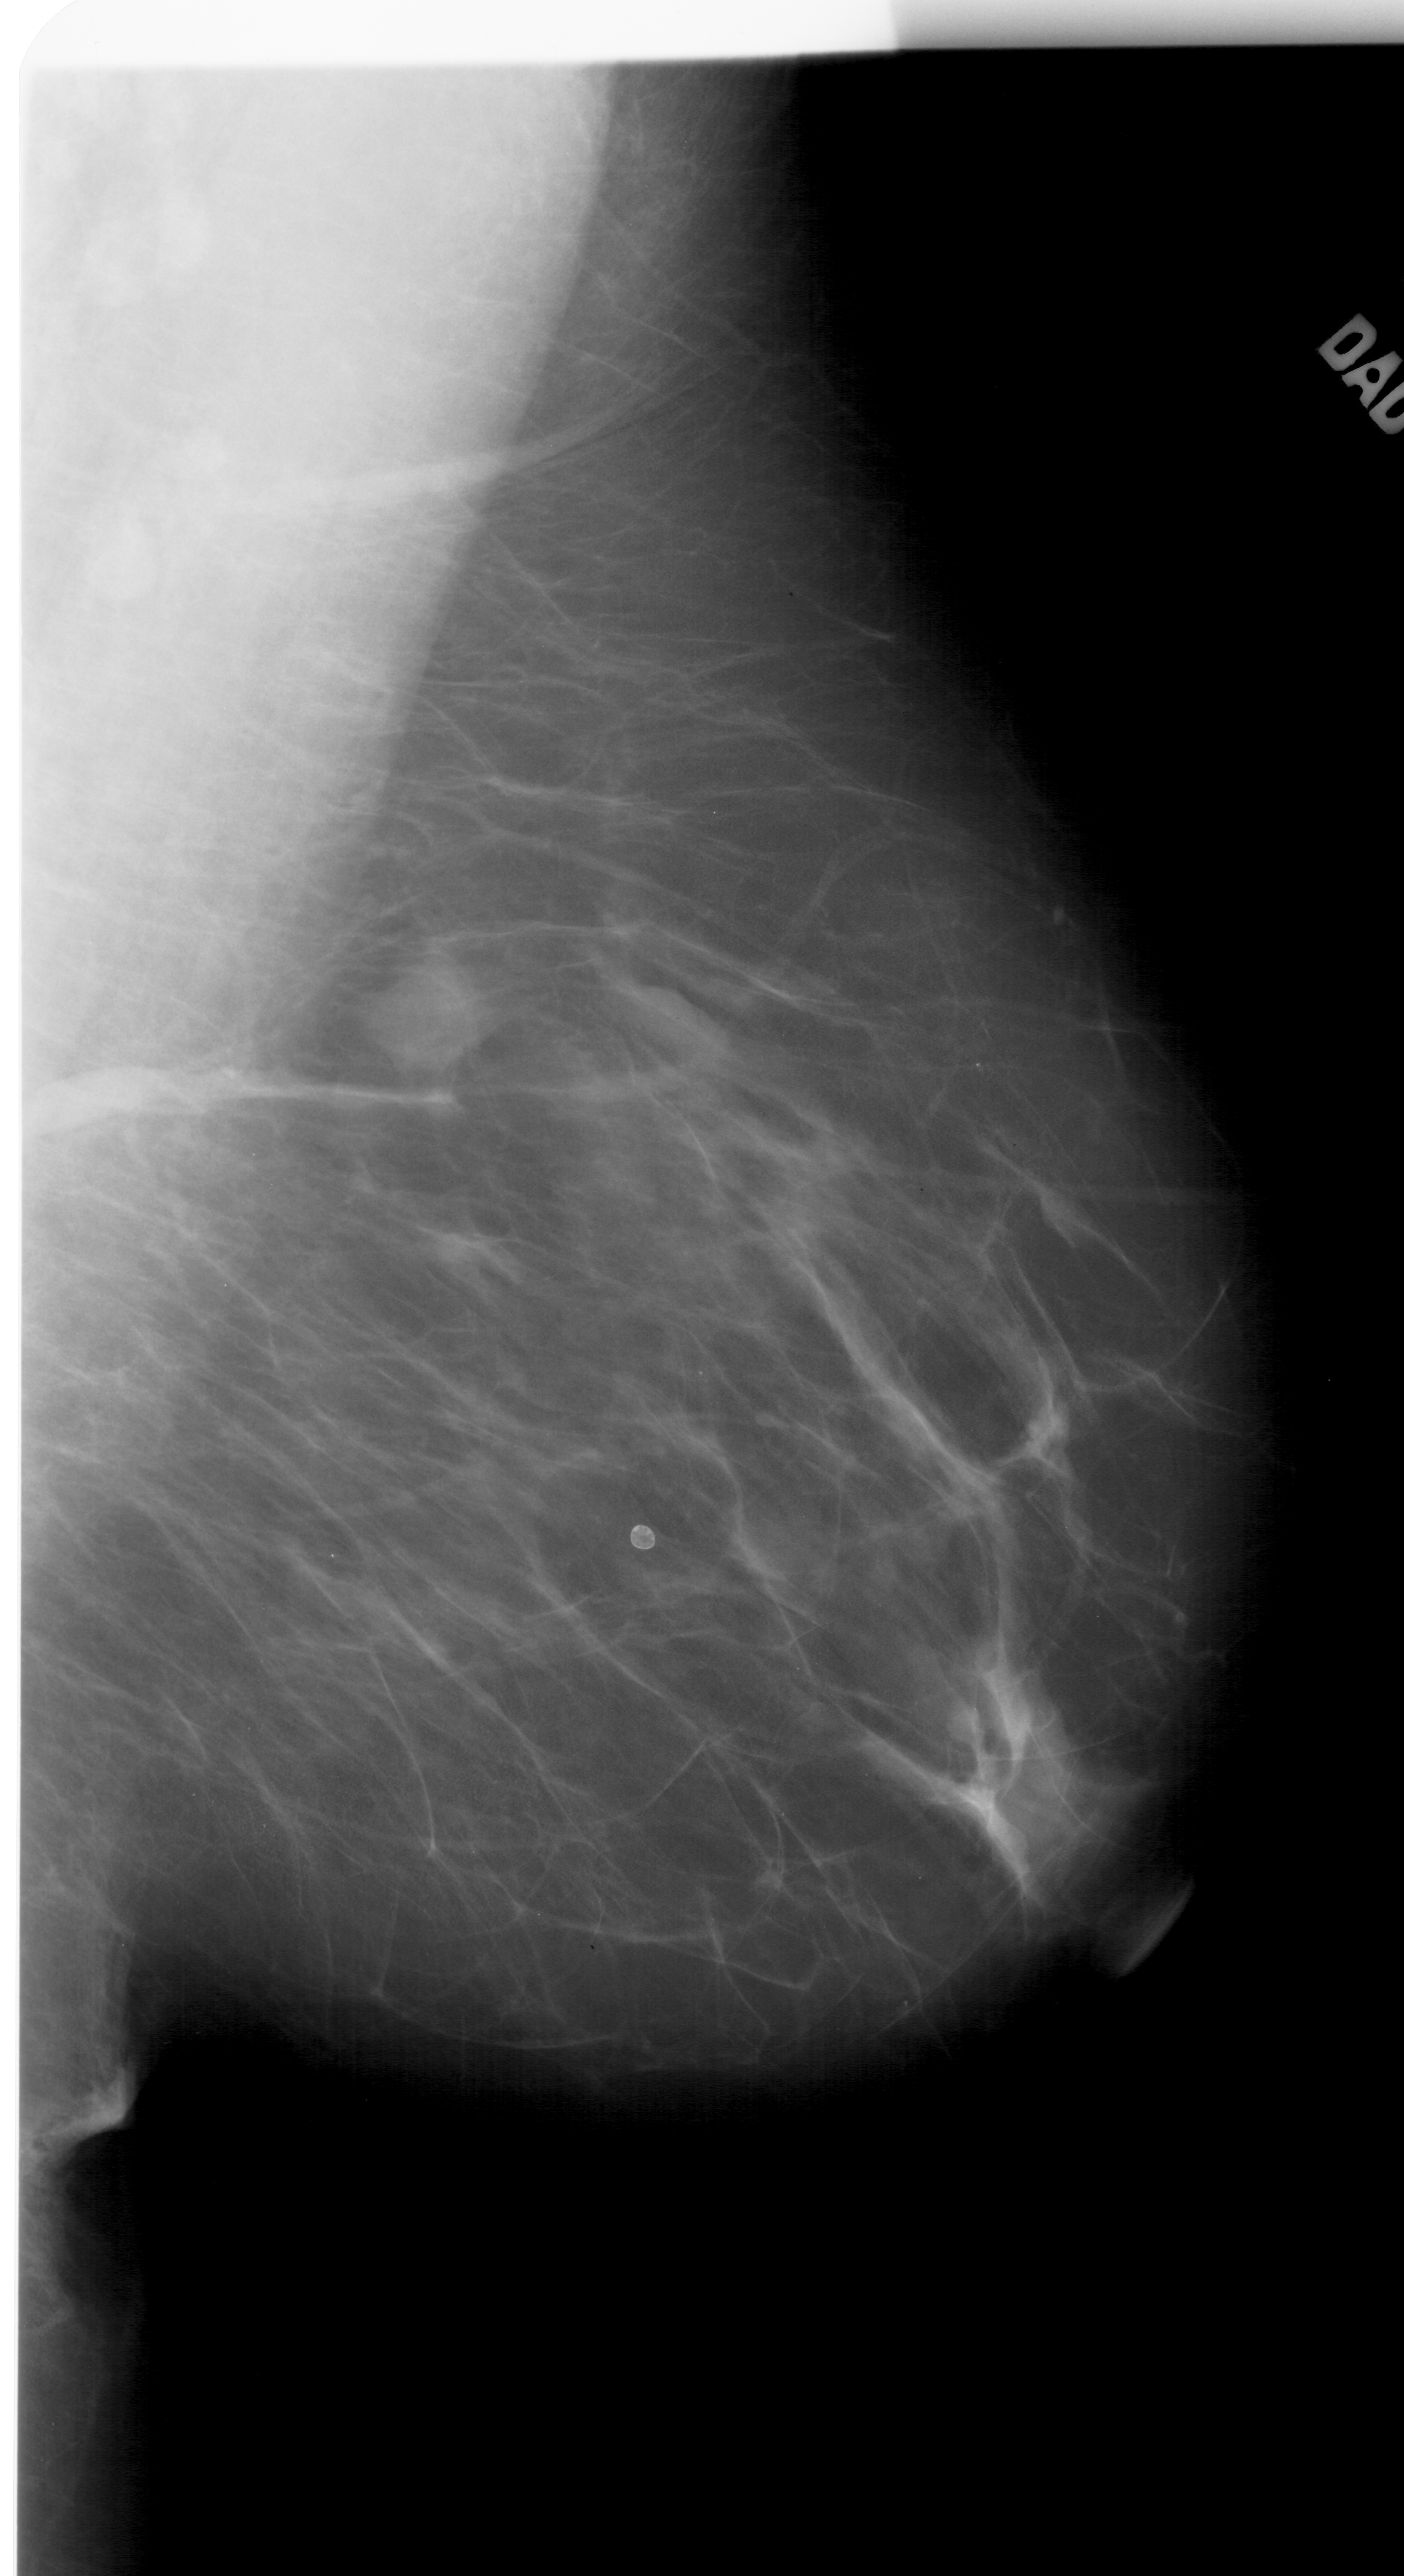
Scanned film-screen mammogram; right breast; mediolateral oblique (MLO) view; BI-RADS breast density category 1 (scale 1–4).
- Finding: mass, shape lobulated, margins ill defined; BI-RADS assessment category 4; pathology (as recorded): benign.